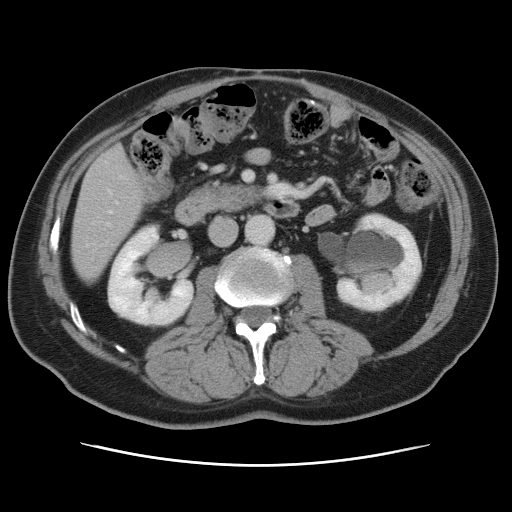
Contrast-enhanced abdominal CT, one axial slice. Slice 24 of 80 in the series (ordered by position). 120 kVp. Intravenous contrast given. Soft-tissue window (W 400 / L 40 HU). 5 mm slice thickness. 512 × 512 image matrix. Male patient, age 69 years. From the clinical record (not read from this slice): diagnosis: colorectal cancer liver metastases, imaged before liver resection; multiple liver metastases: no; largest metastasis: 5 cm.
Annotated regions visible in this slice (outlined manually by an expert reader):
- hepatic veins: bounding box <87,190,117,246> (left, top, right, bottom; pixels)
- liver: <72,148,145,282>
- planned liver remnant (the part of the liver to remain after resection): <72,221,126,282>